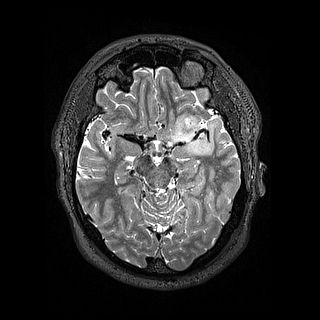
Brain MRI from a brain-tumour surgery series, one axial slice. Slice 96 of 144 in the series (ordered by position). 1.2 mm slice thickness. 320 × 320 image matrix, field of view 254 × 254 mm. Case-level facts recorded for this patient, not image findings: histopathology: Astrocytoma; WHO grade: 2; IDH mutation: yes; tumour location: Left Insular.
Structures marked on this image (manually delineated by an expert):
- tumour: bounding box <171,111,205,156> (left, top, right, bottom; pixels)